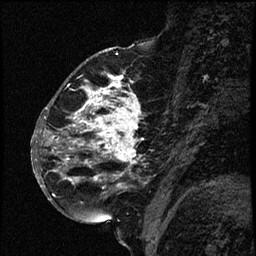
Breast MRI (dynamic contrast-enhanced), one sagittal slice. Position 30 of 66 along the scan axis. Dynamic contrast-enhanced study with each time point stored as its own series, time point 2 of 3 at this slice position (early post-contrast, ordered by acquisition time). 1.5 T. TE 4.2 ms, TR 17.6 ms. 2 mm slice thickness. 256 × 256 image matrix, field of view 200 × 200 mm. Female patient. Case-level facts recorded for this patient, not image findings: setting: breast cancer imaged before/during neoadjuvant chemotherapy; receptor status: HER2-positive.
Outlined on this slice (semi-automatic segmentation, software-assisted and operator-edited):
- analysis volume of interest (the breast-tissue region the enhancement analysis was run in; not a lesion): bounding box (x1, y1, x2, y2) in pixels: (52, 69, 161, 209)
- tumour enhancement mask (voxels above the 100 % enhancement threshold inside the analysis volume of interest): (52, 76, 142, 188)